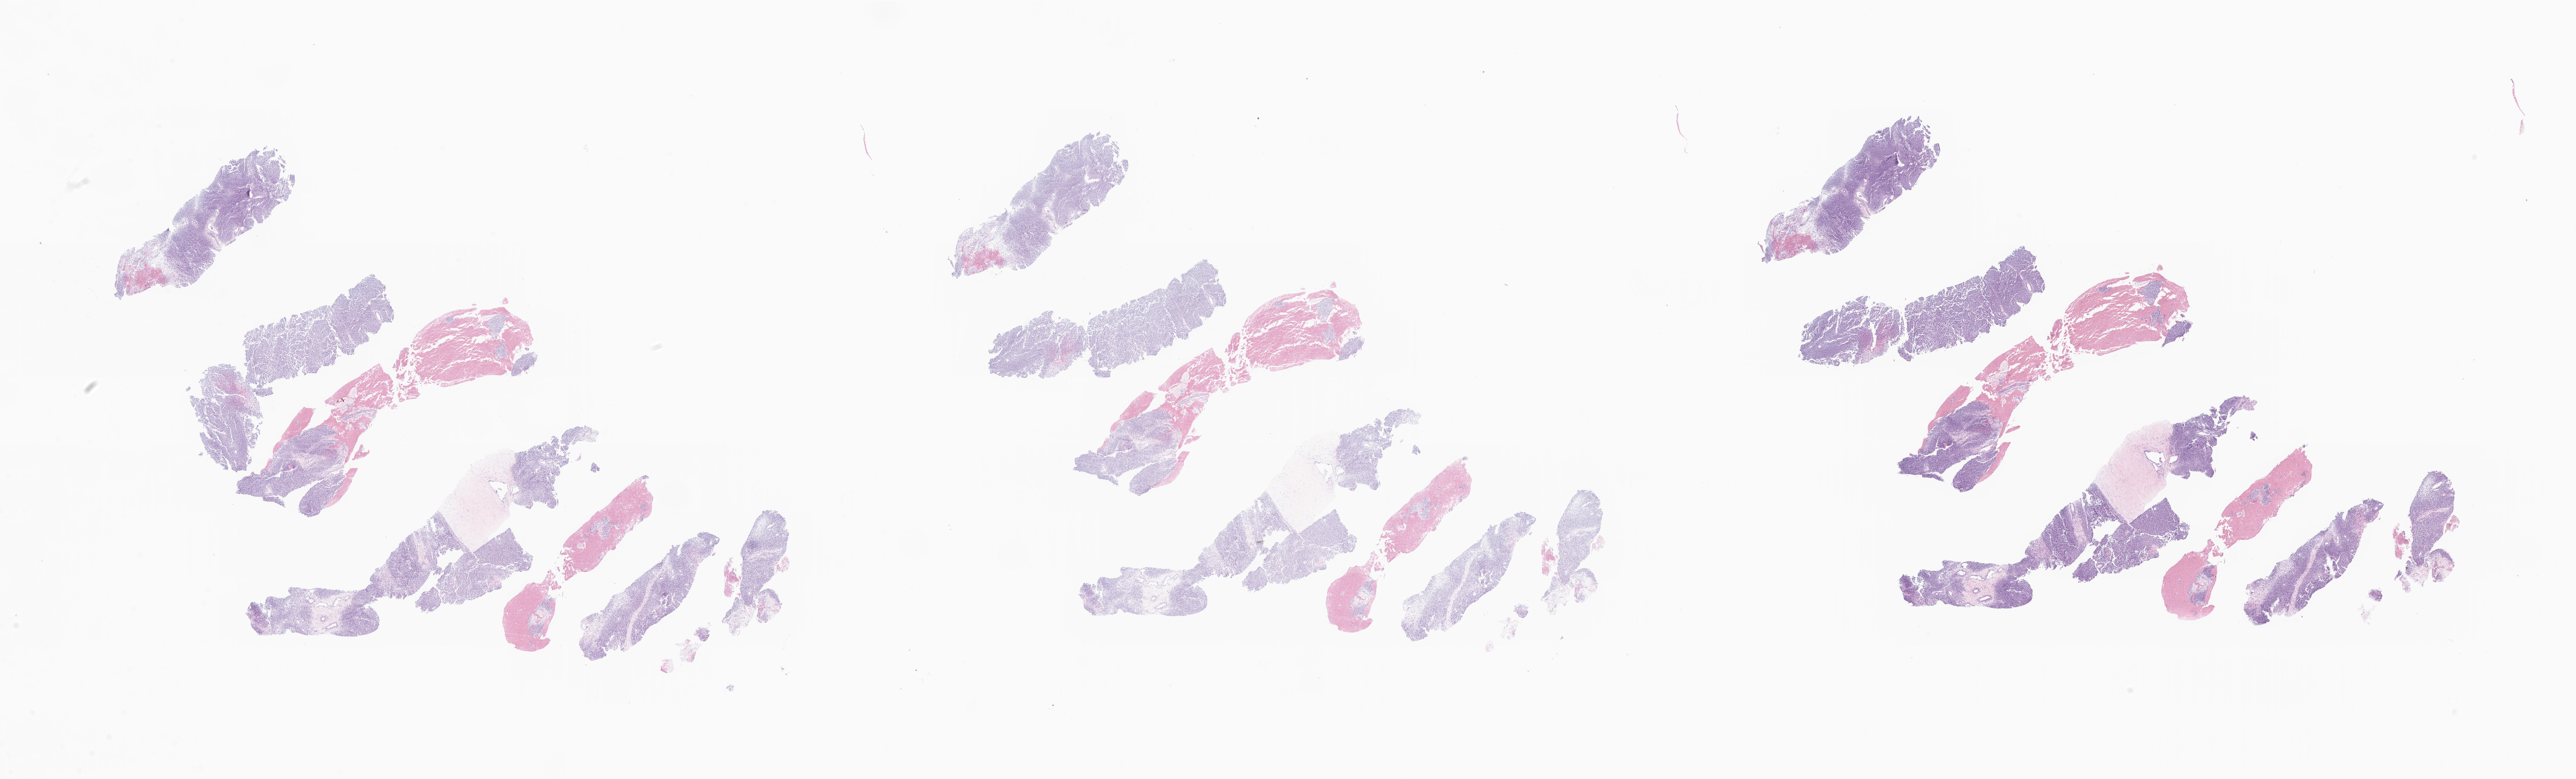
Digitized haematoxylin and eosin-stained section of tumor tissue from the lower limb — shown as a low-resolution overview of the whole scanned area (about 41.0 x 12.4 mm); formalin-fixed, paraffin-embedded (FFPE) tissue. Patient male; age 210 months (17 years 6 months).
Recorded diagnosis: Ewing sarcoma.